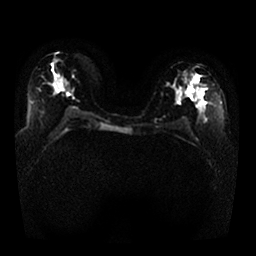
Breast MRI, one axial slice. Position 14 of 25 along the scan axis. Diffusion-weighted series; image 2 of 4 stored at this slice position (different b-values; order by instance number). 1.5 T. 4 mm slice thickness. 256 × 256 image matrix, field of view 350 × 350 mm. Female patient.
Annotated regions visible in this slice (outlined manually by an expert reader):
- tumour on diffusion-weighted imaging: box from (x=188, y=86) to (x=193, y=96) px